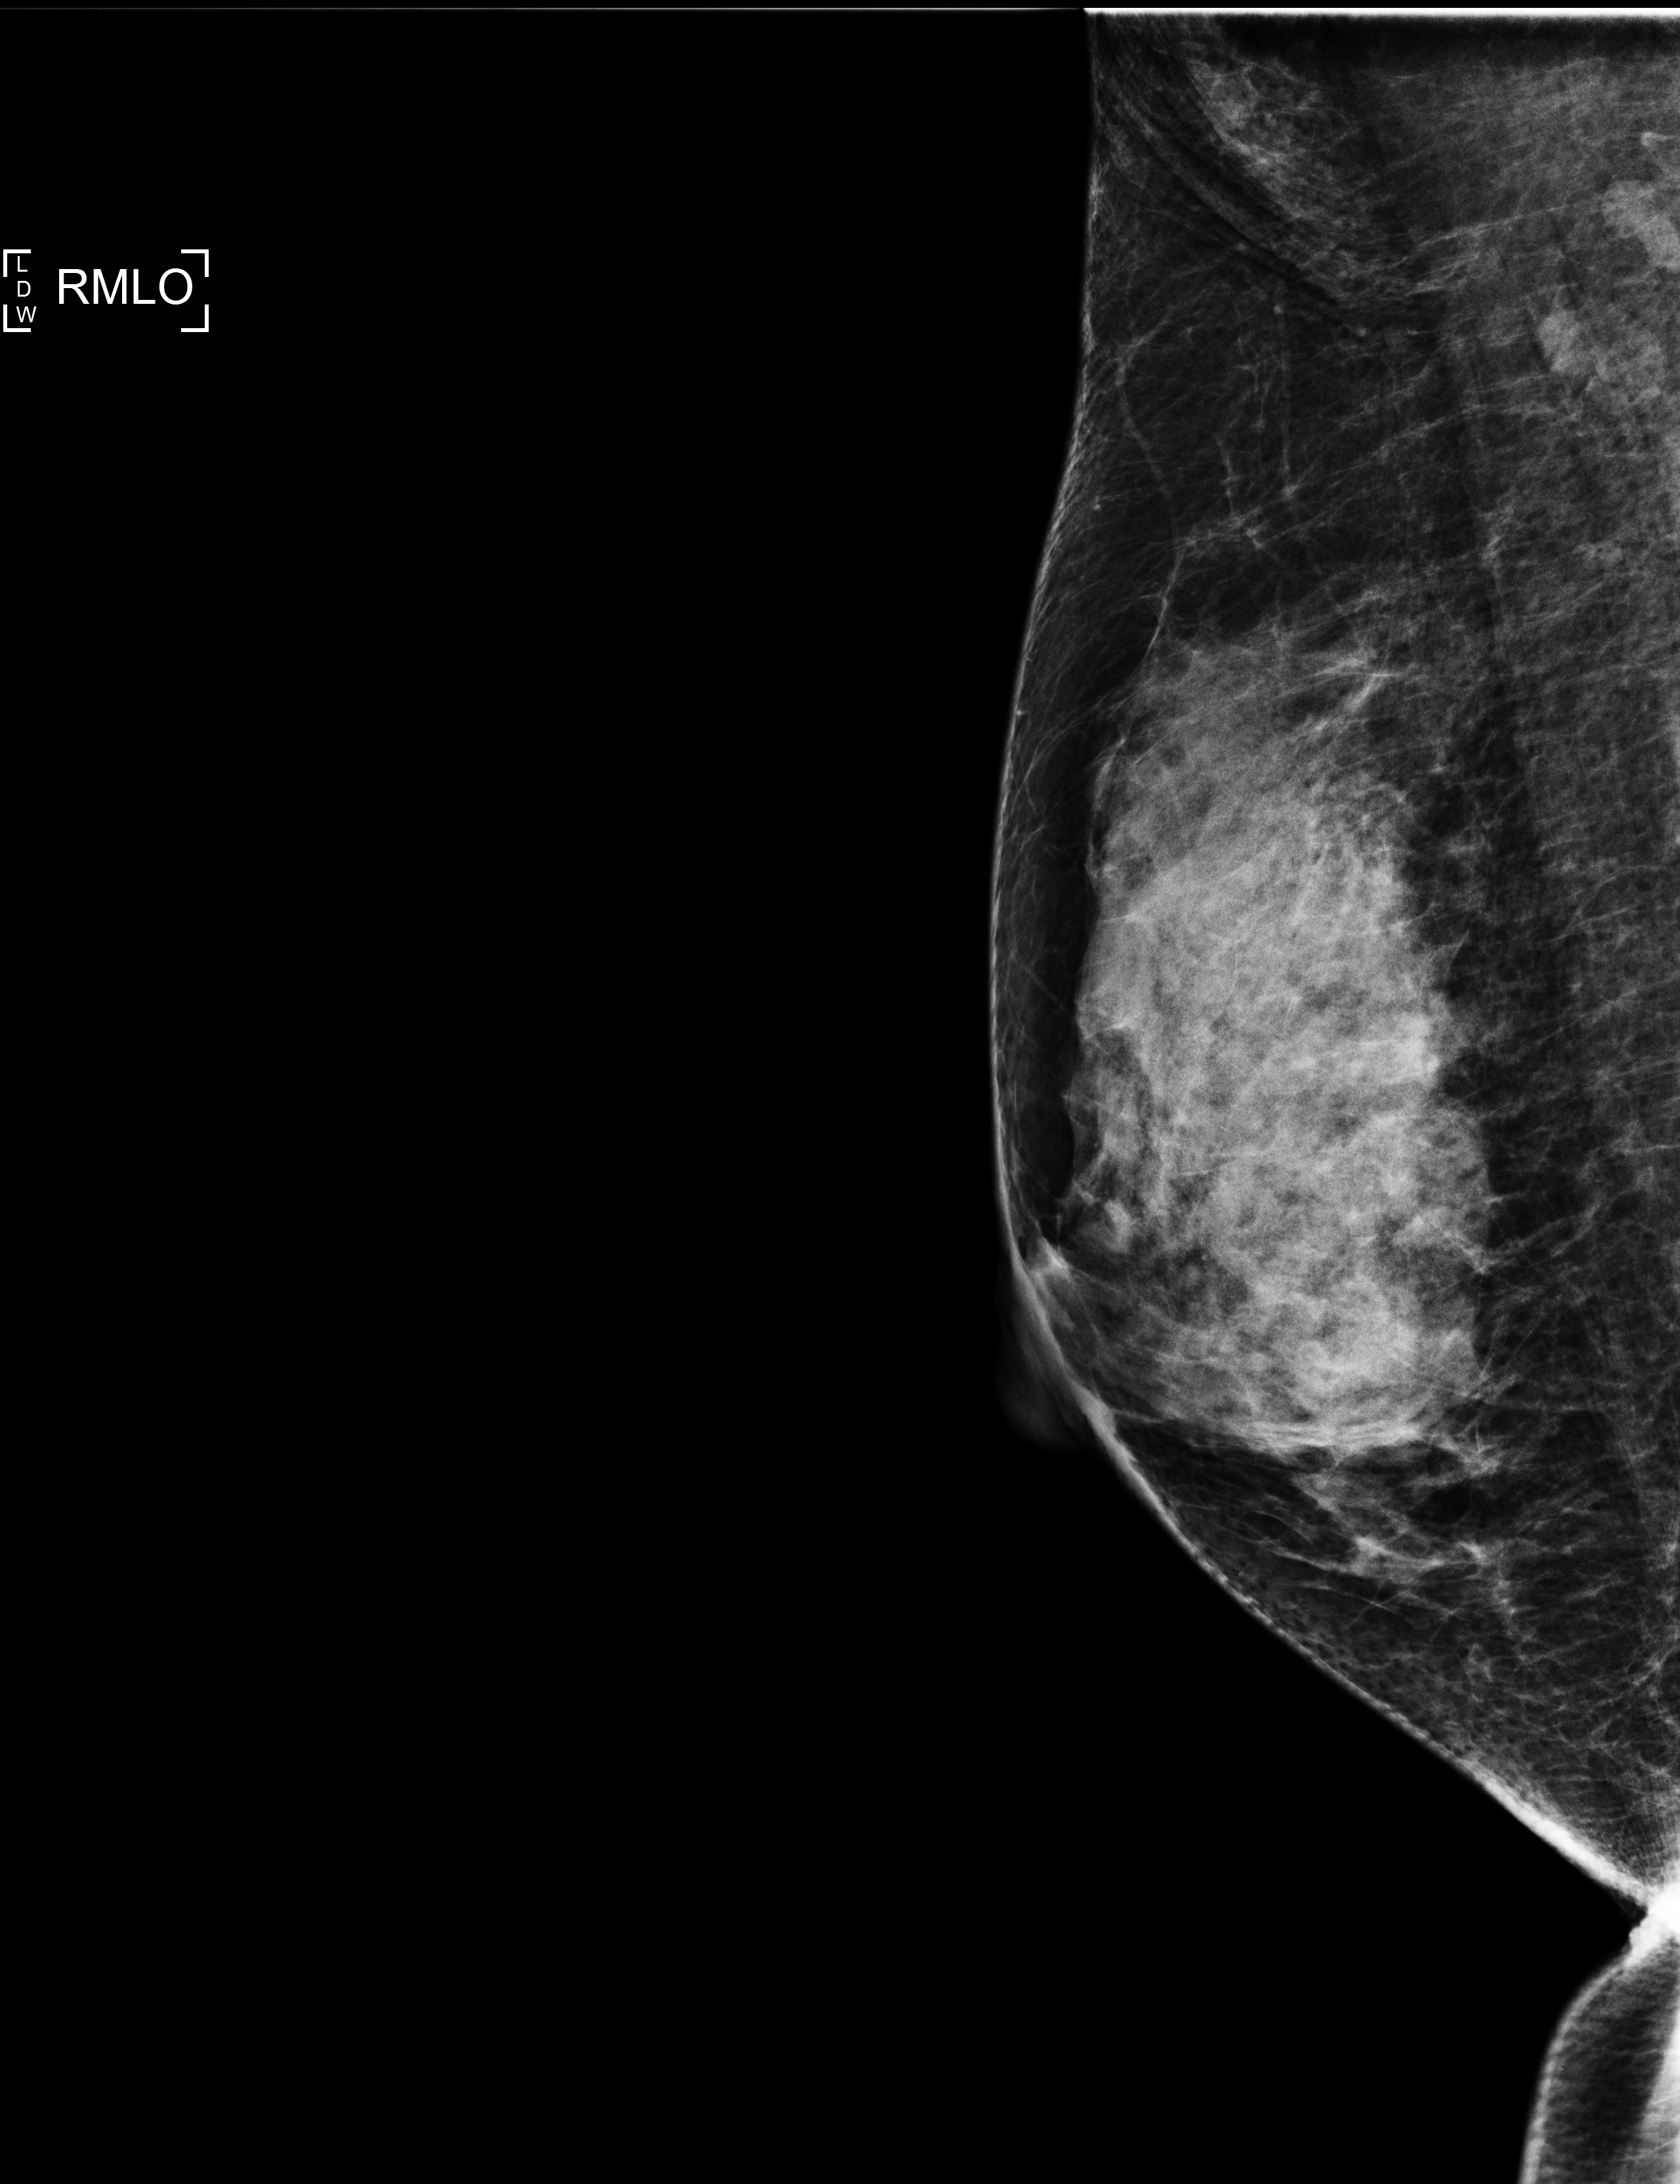
Digital mammogram (FFDM), right breast, mediolateral oblique (MLO) view, screening examination, compressed breast thickness 54 mm, system: Selenia Dimensions. Patient: female, 50 years.
Breast density at the screening exam (both breasts): extremely dense (BI-RADS density category d). Final BI-RADS assessment for this screening round (tomosynthesis exam, both breasts): category 1. Recall: no recall after this screen.